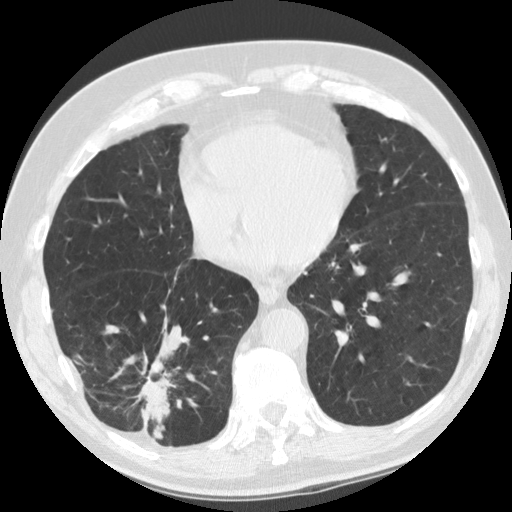
Axial slice from a low-dose chest CT screening exam, baseline screening round, lung window (W 1500 / L -600 HU), standard (soft-tissue) reconstruction kernel (STANDARD), 512 × 512 image matrix. Male, age 69 years at enrolment.
• Expert-annotated lung lesion, box from (x=102, y=330) to (x=188, y=439) px.
• The screening reader recorded 2 non-calcified nodules or masses ≥4 mm on this exam; which of them this box marks is not recorded.